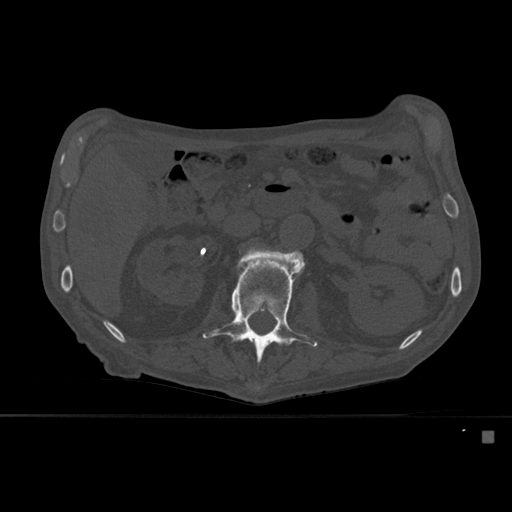
CT including the spine, one axial slice. Slice 236 of 527 in the series (ordered by position). Bone window (W 1800 / L 400 HU). 1.5 mm slice thickness. 512 × 512 image matrix, field of view 373 × 373 mm. Male patient, age 78 years. Case-level facts recorded for this patient, not image findings: primary cancer: prostate.
Annotated regions visible in this slice (semi-automatic segmentation, software-assisted and operator-edited):
- L2 vertebra: bounding box [x1, y1, x2, y2] px = [202, 247, 318, 363]